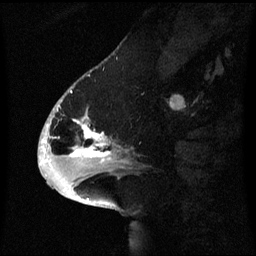
Breast MRI (dynamic contrast-enhanced), one sagittal slice; slice 23 of 60 in the series (ordered by position); dynamic contrast-enhanced series, image 2 of 3 at this slice position (ordered by acquisition); 1.5 T; TE 4.2 ms, TR 8.4 ms; 2.1 mm slice thickness; 256 × 256 image matrix, field of view 220 × 220 mm. Female patient, age 53 years. From the clinical record (not read from this slice): setting: breast cancer imaged before/during neoadjuvant chemotherapy; receptor status: HR-positive, HER2-negative.
Annotated regions visible in this slice (semi-automatic segmentation, software-assisted and operator-edited):
- analysis volume of interest (the breast-tissue region the enhancement analysis was run in; not a lesion): bounding box (x1, y1, x2, y2) in pixels: (52, 90, 131, 171)
- tumour enhancement mask (voxels above the 70 % enhancement threshold inside the analysis volume of interest): (57, 104, 112, 161)